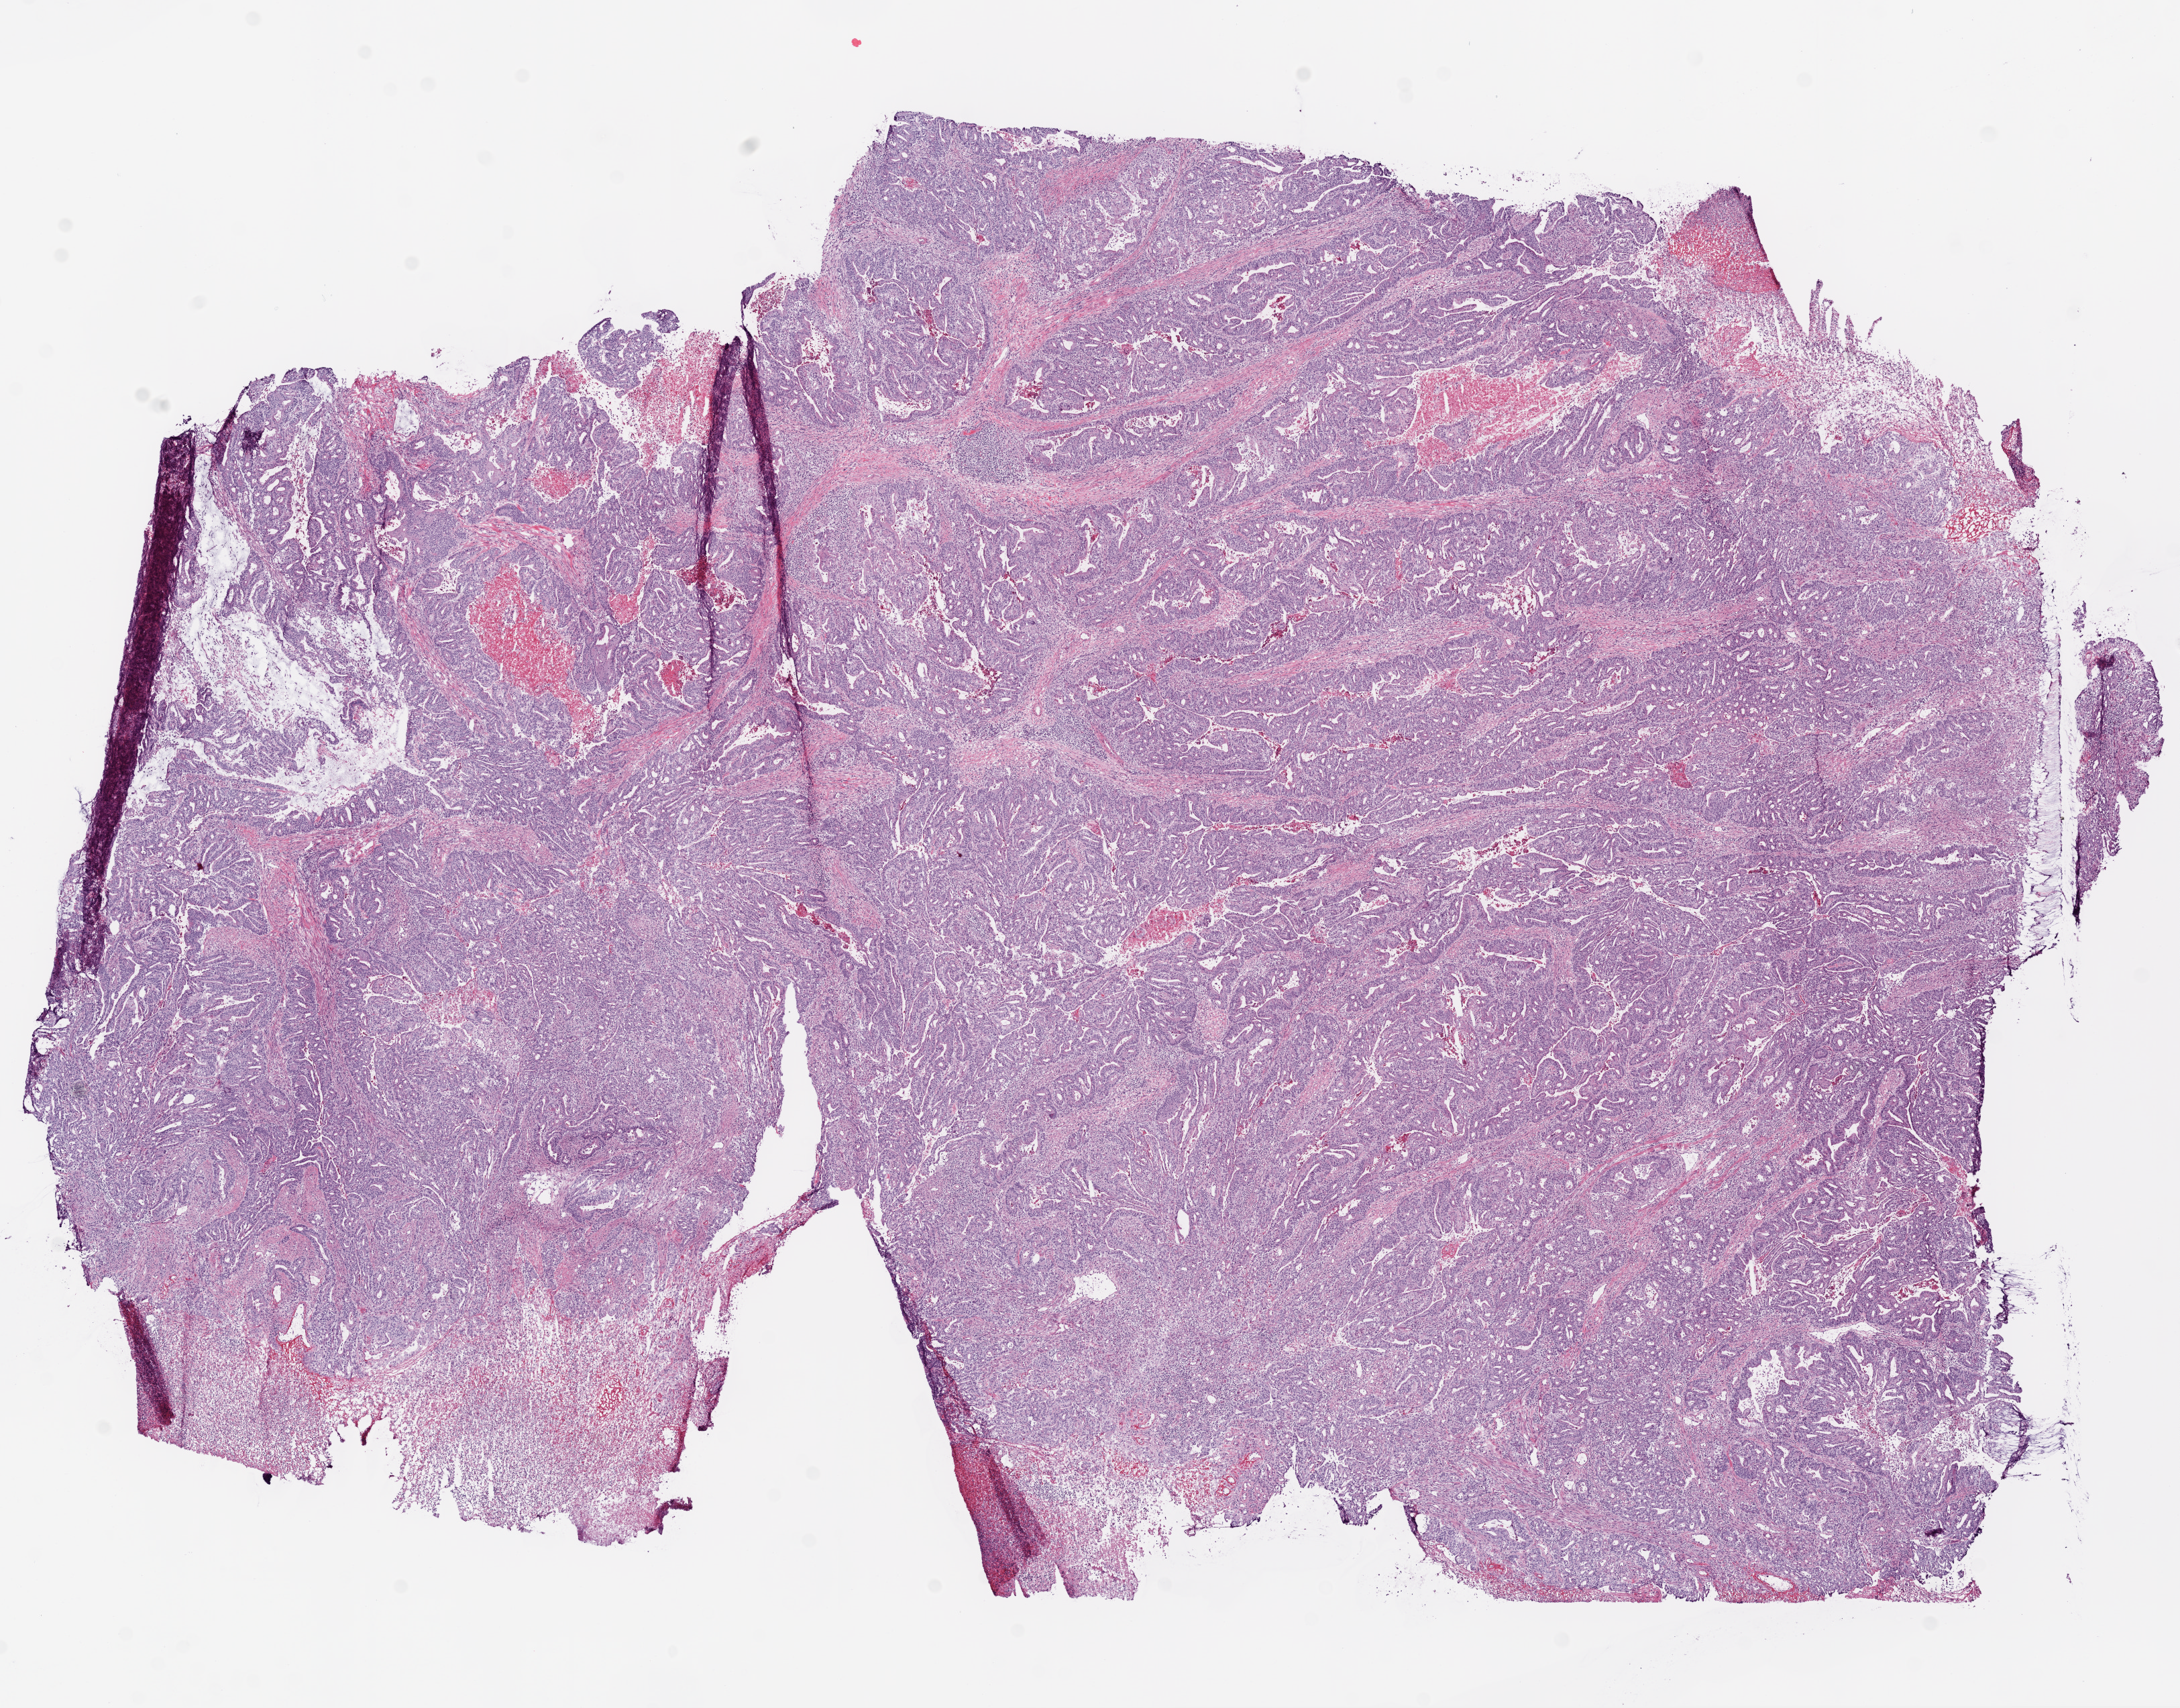
Whole-slide histology image, H&E — whole scanned area (about 13.0 x 10.2 mm) shown as a low-resolution overview; frozen section from the bottom of the tissue portion; colon, primary tumour sample. Patient: female, age at initial diagnosis 82 years. Slide review estimates, as recorded: tumour cells 90%, tumour nuclei 80%, normal cells 0%, stromal cells 5%, necrosis 5%.
- AJCC pathologic stage: IIIB
- lymph nodes positive (case pathology): 1 of 29 examined
- histologic diagnosis: Adenocarcinoma, NOS (ascending colon)